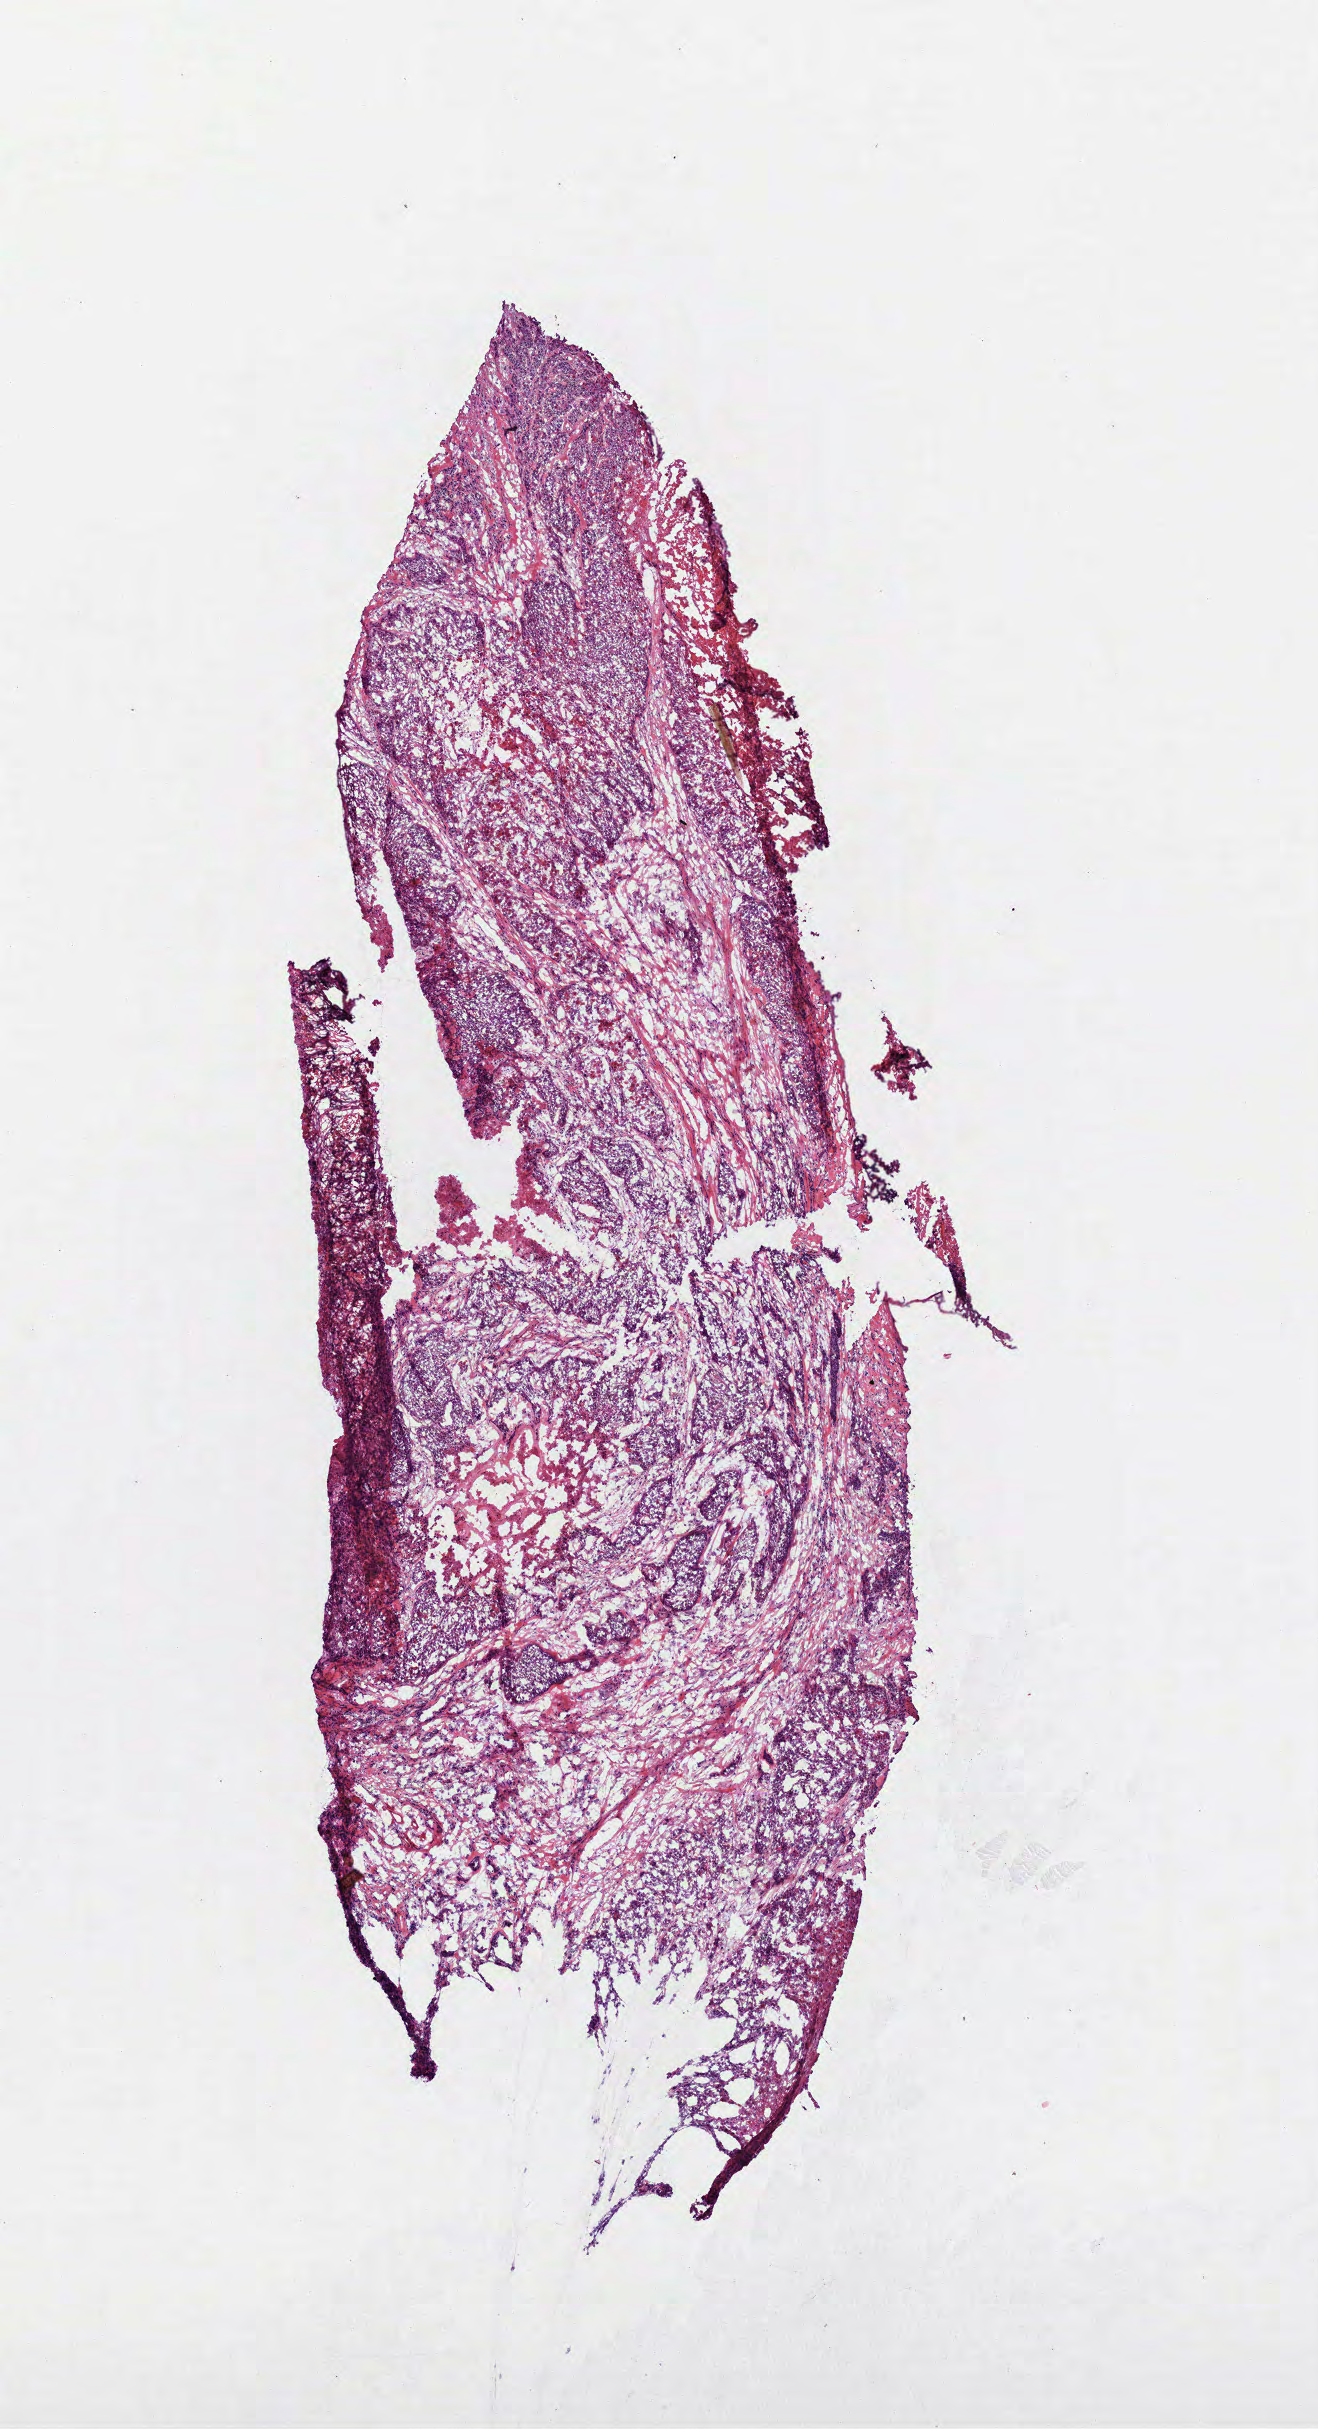
Digitized Hematoxylin and eosin (H&E) stained tissue section (whole slide) — whole scanned area (about 5.3 x 9.8 mm, acquisition: 40x scan) shown as a low-resolution overview, frozen section from the bottom of the tissue portion, sample: primary tumour, head and neck. Male patient; age at initial diagnosis 67 years. Histologic grade: G3 (poorly differentiated). Slide review estimates, as recorded: tumour cells 85%, tumour nuclei 80%, normal cells 0%, stromal cells 0%, necrosis 15%. Inflammatory infiltration, as recorded: lymphocyte infiltration 5%, monocyte infiltration 0%, neutrophil infiltration 0%.
* AJCC pathologic stage: IVA (7th edition)
* histologic diagnosis: Squamous cell carcinoma, NOS
* TNM: T3 N2c